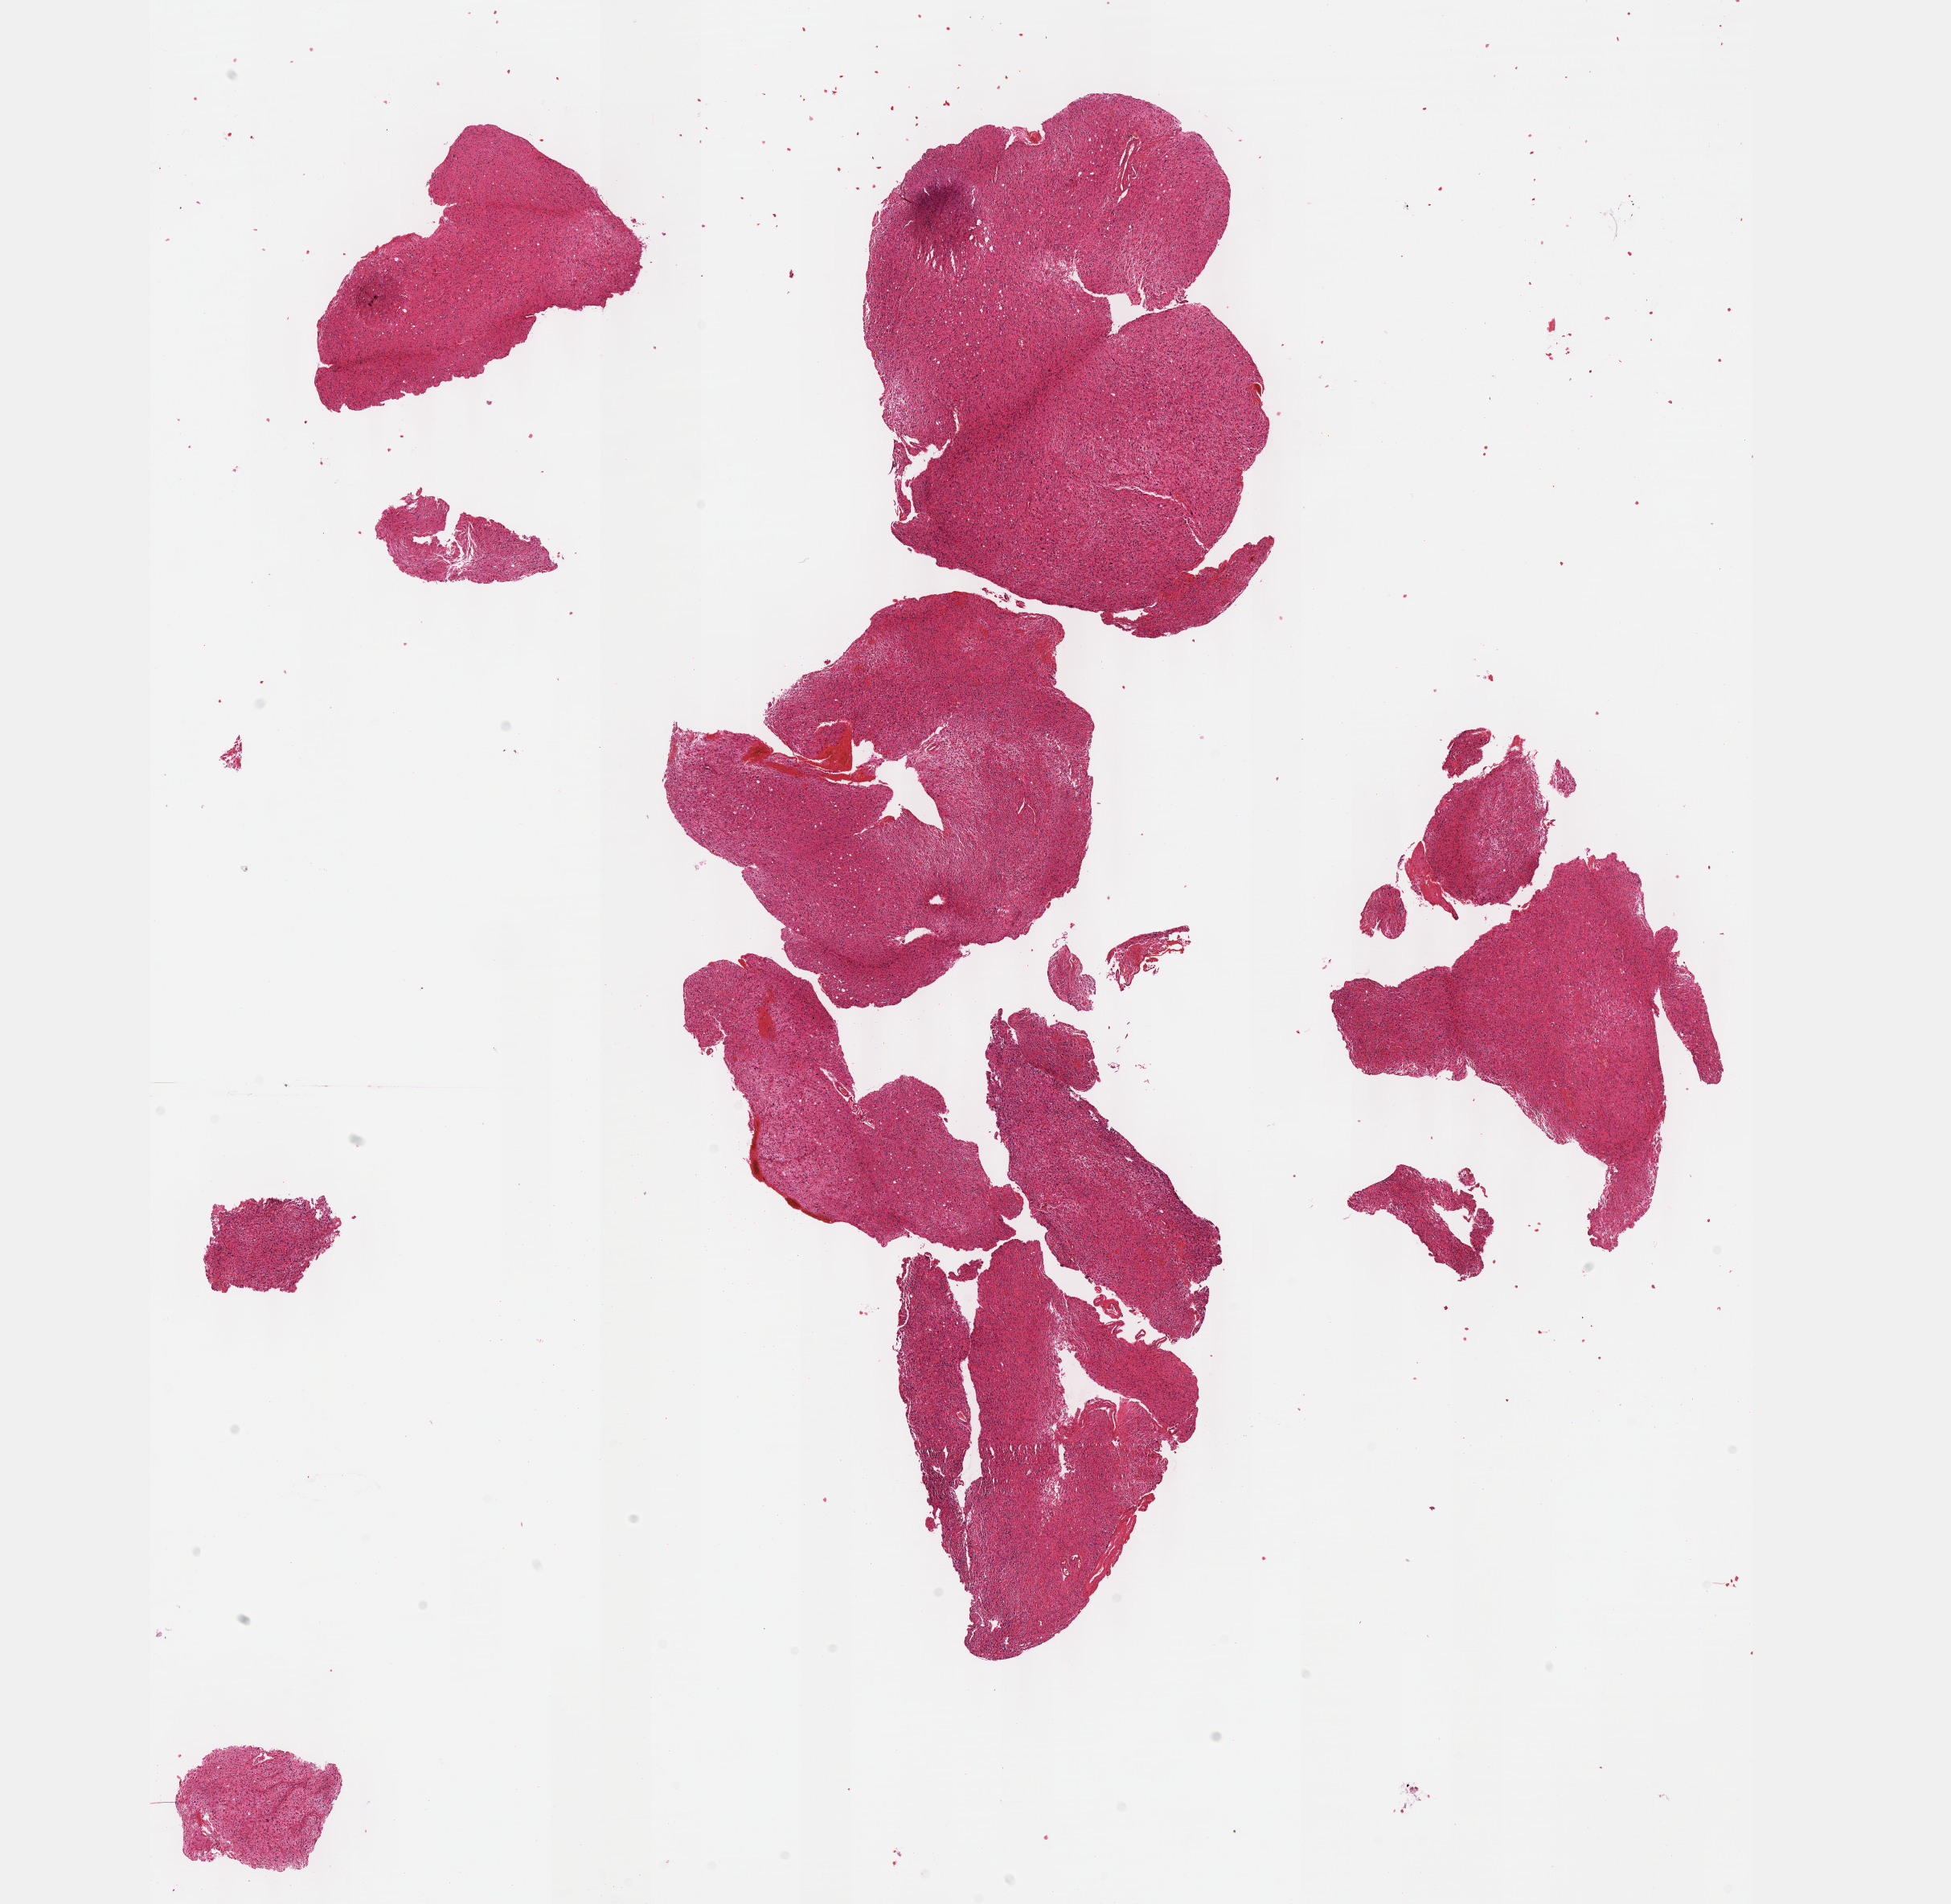
Digitized H&E-stained tissue section (whole slide), a low-resolution overview of the entire scanned area, about 19.6 x 19.1 mm (from a 40x scan); FFPE section; brain, primary tumour sample. Patient: male, age at initial diagnosis 40 years.
Histologic diagnosis: Astrocytoma, anaplastic (cerebrum).